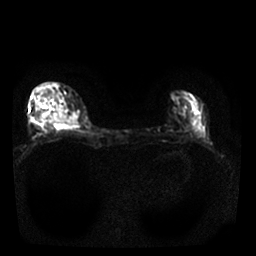
Breast MRI, one axial slice; position 11 of 25 along the scan axis; diffusion-weighted series; image 2 of 4 stored at this slice position (different b-values; order by instance number); 1.5 T; 4 mm slice thickness; 256 × 256 image matrix. Female patient.
Annotated regions visible in this slice (outlined manually by an expert reader):
- tumour on diffusion-weighted imaging: bounding box <51,115,76,125> (left, top, right, bottom; pixels)